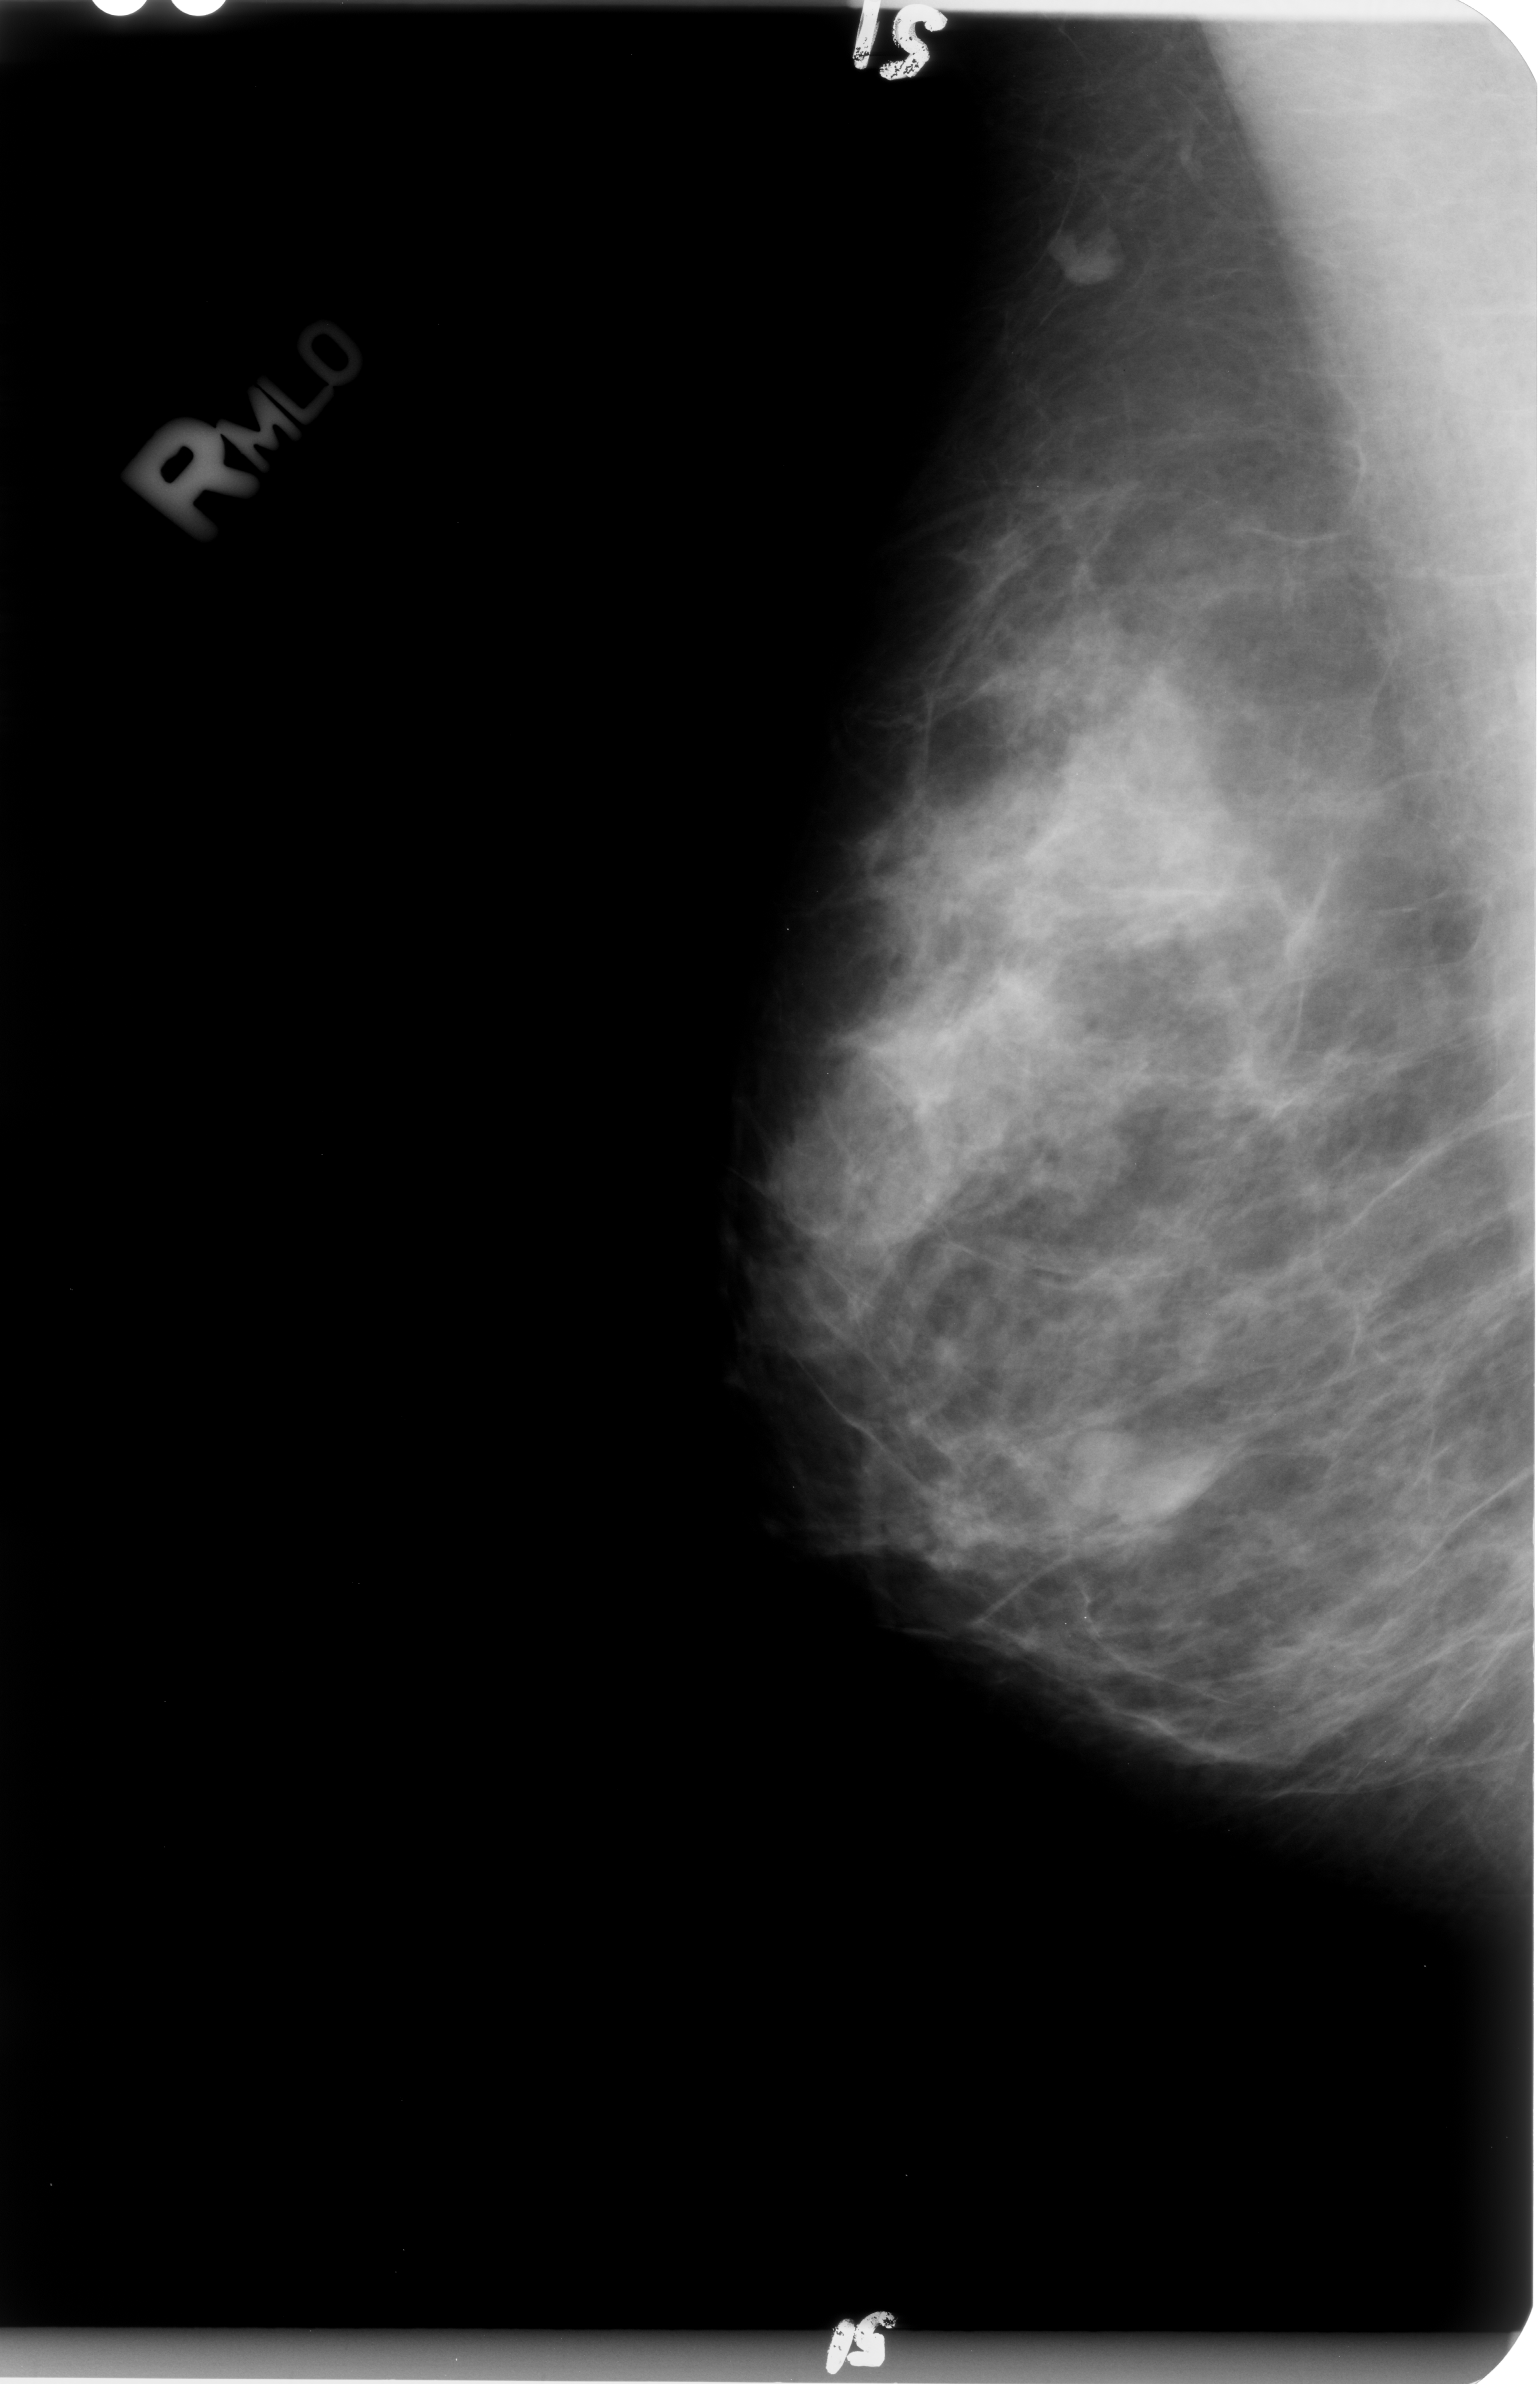
Mammogram (digitized film), right breast, mediolateral oblique (MLO) view, breast composition: heterogeneously dense (BI-RADS density category 3 of 4).
Mass, shape irregular, margins circumscribed / ill defined; BI-RADS assessment category 4; subtlety rating 4 on a 1 (subtle) to 5 (obvious) scale; pathology (as recorded): benign.